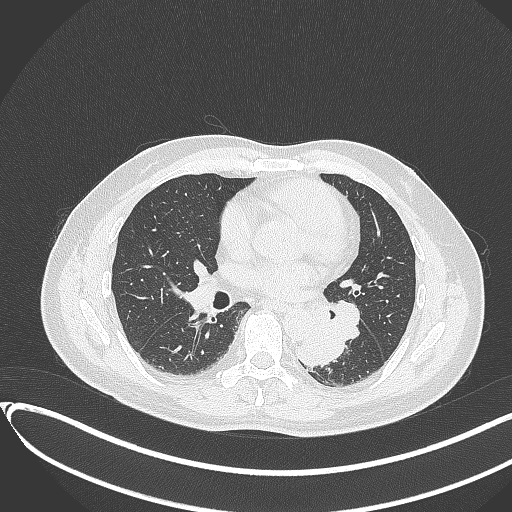
Chest CT, one axial slice; position 170 of 417 along the scan axis; reconstruction kernel B70f; lung window (W 1500 / L -600 HU); 1 mm slice thickness; 512 × 512 image matrix, field of view 400 × 400 mm. Patient: male, 54 years. Case-level facts recorded for this patient, not image findings: clinical TNM (as recorded): T3 N0 M0.
Structures marked on this image (bounding box drawn by a radiologist):
- lung tumour (recorded histology: squamous cell carcinoma): bounding box [x1, y1, x2, y2] px = [287, 318, 350, 368]